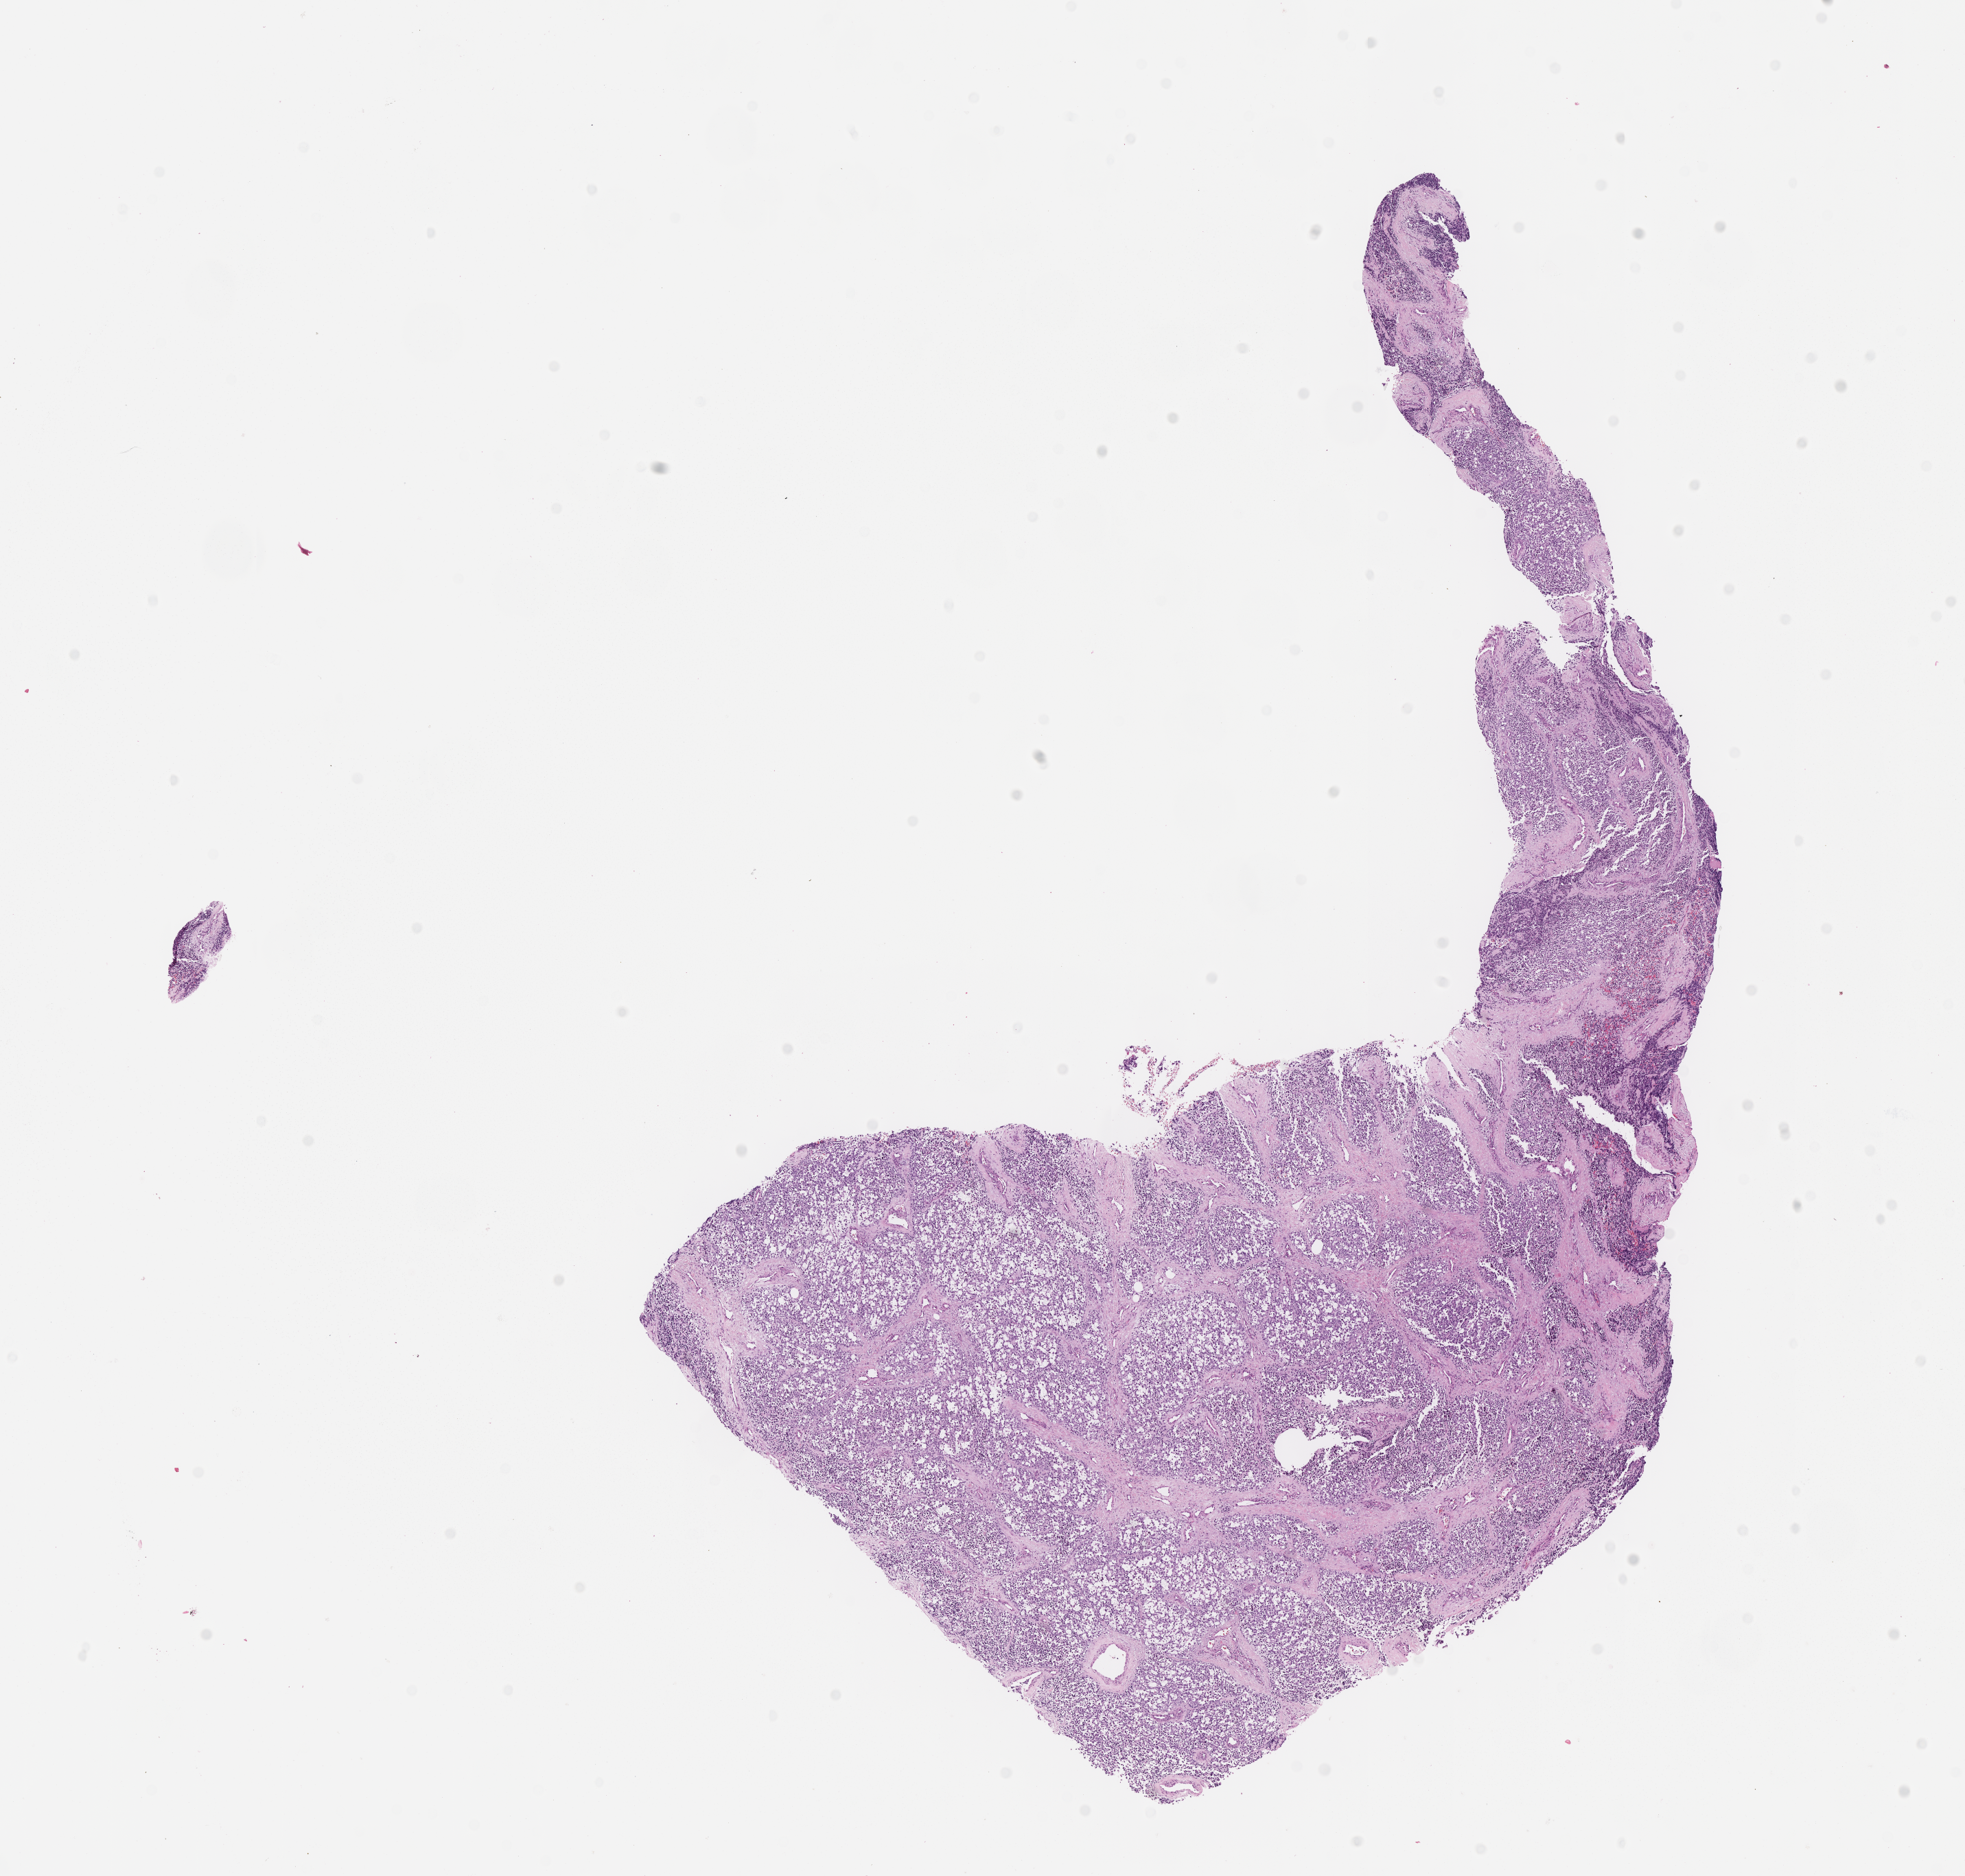
Whole-slide image, H&E stain of tumor tissue — shown as a low-resolution overview of the whole scanned area (about 11.6 x 11.1 mm). FFPE section. Sample anatomic site: pelvis. Patient: male, age 8.2 years at diagnosis.
- diagnosis: rhabdomyosarcoma; histological classification: embryonal rhabdomyosarcoma
- stage (as recorded): 3
- metastatic status at presentation (as recorded): non-metastatic (unconfirmed)